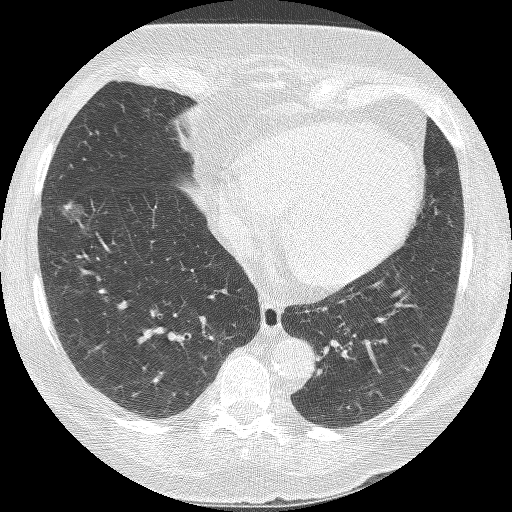
Axial slice from a low-dose chest CT screening exam, second annual screen, lung window (W 1500 / L -600 HU), 1.25 mm slice thickness, slice 95 of 245 in the series, 512 × 512 image matrix. Female participant, aged 68 years at enrolment. Current smoker at enrolment.
Expert reader's lesion annotation, bounding box <34,193,89,249> (left, top, right, bottom; pixels). The exam's reader record, not a measurement of the box and not confirmed to be the same lesion: non-calcified nodule or mass ≥4 mm, right lower lobe, 18 × 15 mm, poorly defined margins, ground glass attenuation, pre-existing on the prior screen: yes; interval growth: yes. Official screen result: positive, other.